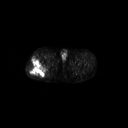
FDG PET of an extremity soft-tissue mass (from a PET/CT study), one axial slice; slice 258 of 267 in the series (ordered by position); 3.27 mm slice thickness; 128 × 128 image matrix, field of view 700 × 700 mm. Male patient, age 43 years. Case-level facts recorded for this patient, not image findings: histological type: poorly differentiated synovial sarcoma; grade: high; site of the primary tumour: right buttock.
Structures marked on this image (expert contour drawn on MRI and transferred to this co-registered scan by the dataset authors):
- gross tumour volume including surrounding oedema: bounding box <27,57,47,78> (left, top, right, bottom; pixels)
- gross tumour volume (mass): <27,57,47,78>